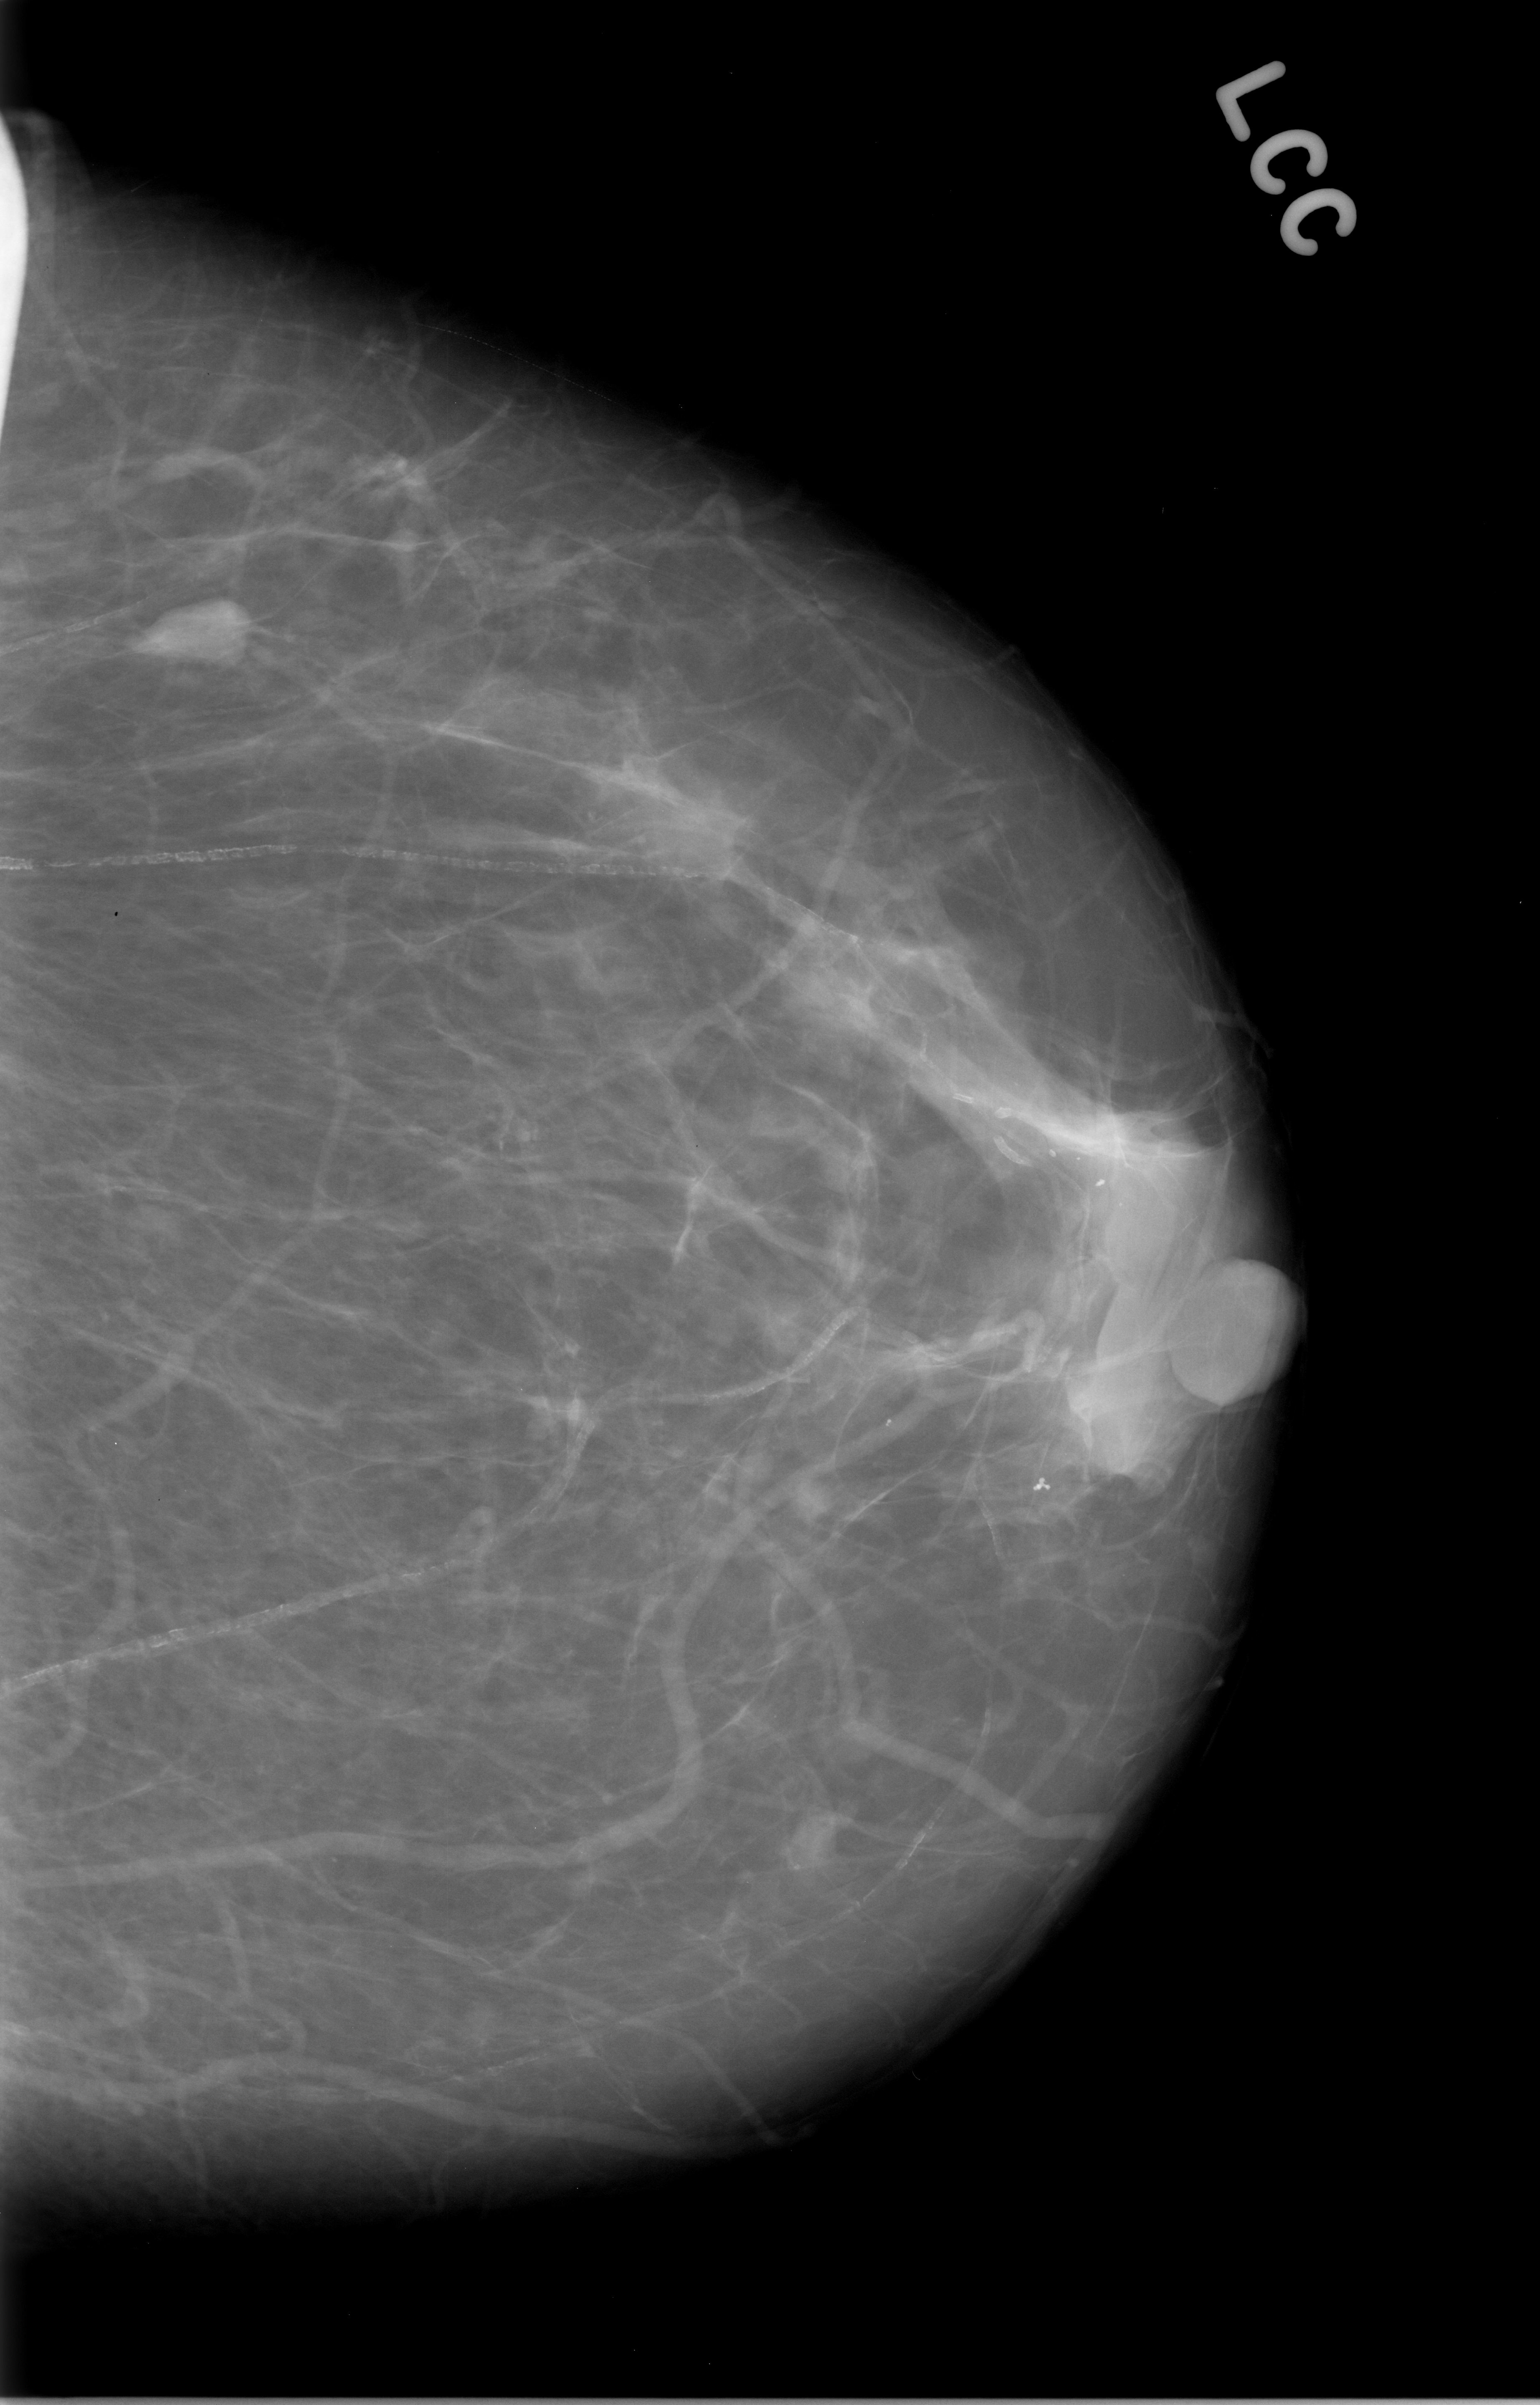
Mammogram (digitized film). Left breast. Craniocaudal (CC) view. BI-RADS breast density category 1 (scale 1–4). 1540 × 2405 image matrix.
Expert-marked regions of interest on this film, with their recorded descriptors:
- mass, shape oval, margins circumscribed; BI-RADS assessment category 2; pathology result (as recorded, not read from the image): benign: box from (x=116, y=581) to (x=264, y=676) px